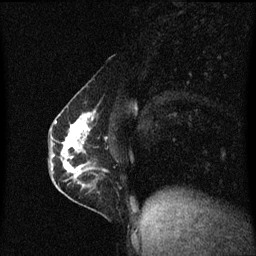
Breast MRI (dynamic contrast-enhanced), one sagittal slice; position 26 of 60 along the scan axis; dynamic contrast-enhanced series, image 2 of 3 at this slice position (ordered by acquisition); 1.5 T; TE 4.2 ms, TR 8.4 ms; 2 mm slice thickness; 256 × 256 image matrix. Patient: female, 40 years.
Structures marked on this image (semi-automatically segmented with operator editing):
- analysis volume of interest (the breast-tissue region the enhancement analysis was run in; not a lesion): bounding box (x1, y1, x2, y2) in pixels: (57, 110, 104, 191)
- tumour enhancement mask (voxels above the 70 % enhancement threshold inside the analysis volume of interest): (61, 112, 95, 183)